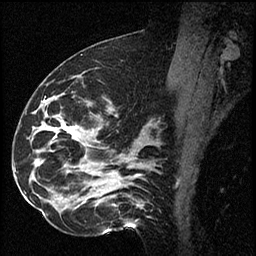
Breast MRI (dynamic contrast-enhanced), one sagittal slice; slice 34 of 60 in the series (ordered by position); dynamic contrast-enhanced series, image 2 of 2 at this slice position (ordered by acquisition); 1.5 T; TE 4.2 ms, TR 17.3 ms; 2 mm slice thickness; 256 × 256 image matrix. Female patient. From the clinical record (not read from this slice): setting: breast cancer imaged before/during neoadjuvant chemotherapy; receptor status: HR-positive, HER2-negative.
Outlined on this slice (semi-automatic segmentation, software-assisted and operator-edited):
- analysis volume of interest (the breast-tissue region the enhancement analysis was run in; not a lesion): box from (x=41, y=95) to (x=115, y=223) px
- tumour enhancement mask (voxels above the 100 % enhancement threshold inside the analysis volume of interest): (x=69, y=130)–(x=76, y=139)